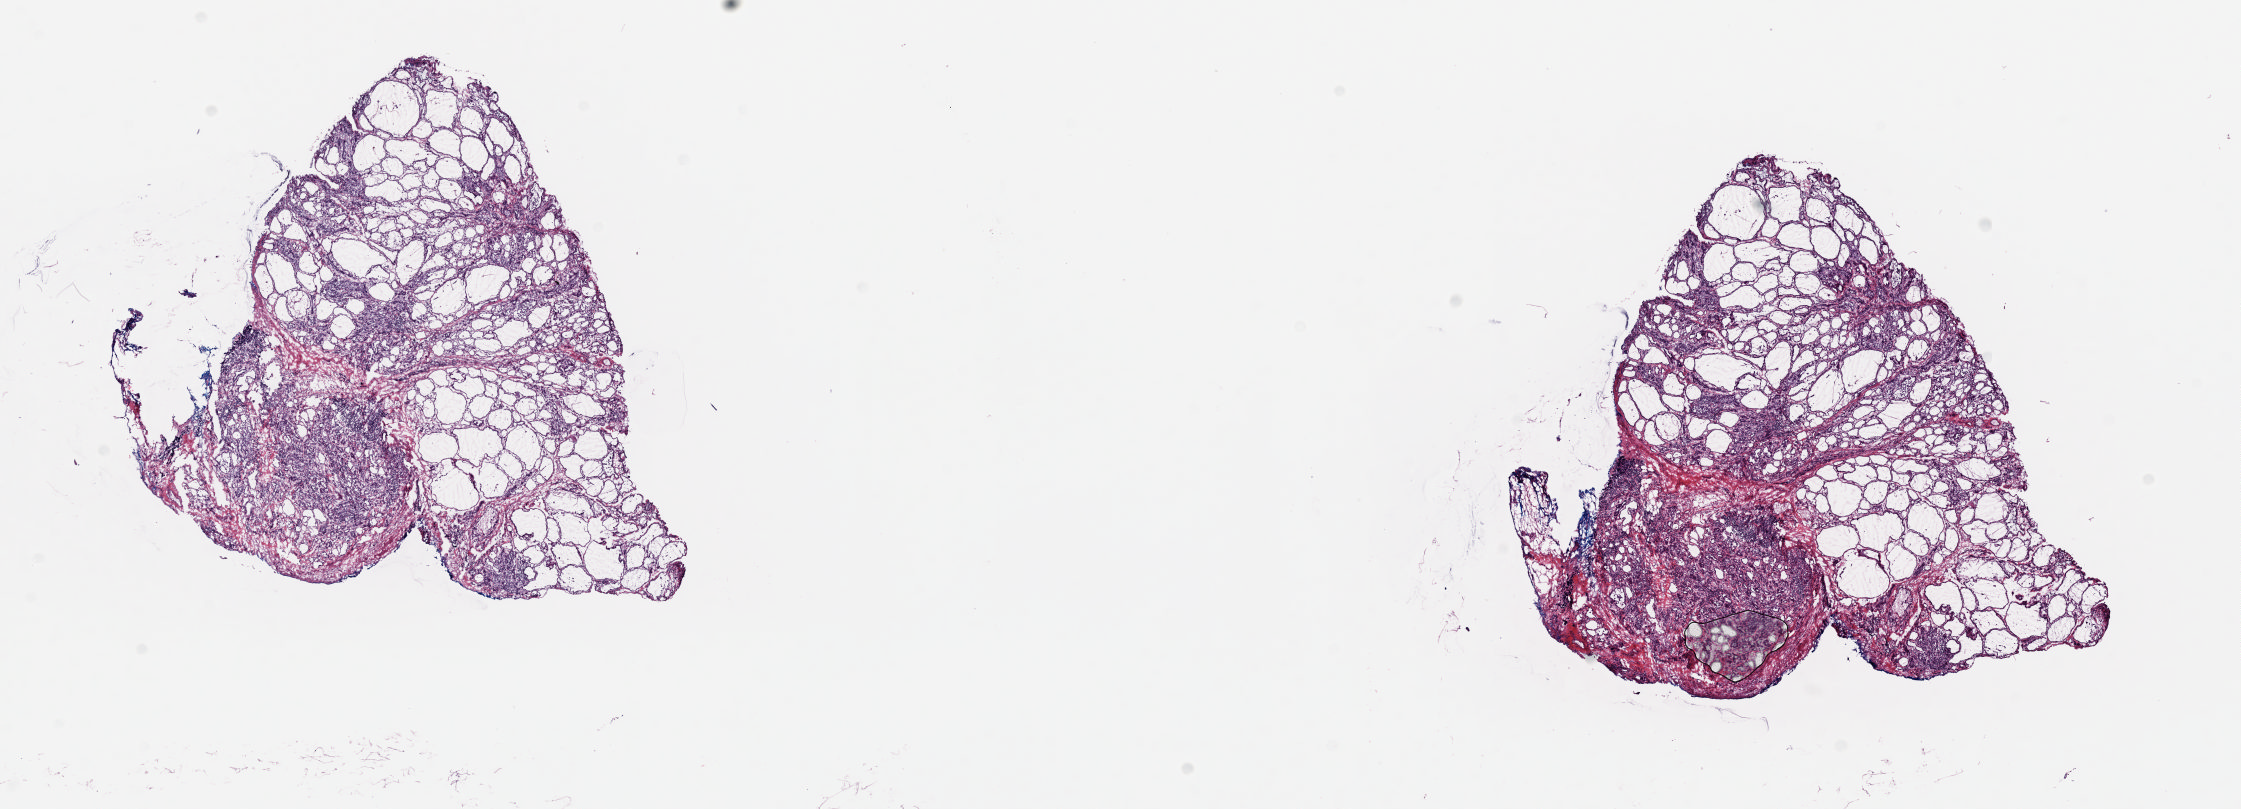
Whole-slide histology image, H&E, whole scanned area (about 17.7 x 6.4 mm) shown as a low-resolution overview; frozen section from the top of the tissue portion; thyroid, solid tissue normal (non-tumour tissue) sample. Female, age 33 years at initial diagnosis. Slide review estimates, as recorded: tumour cells 0%, tumour nuclei 0%, normal cells 70%, stromal cells 30%, necrosis 0%. Inflammatory infiltration, as recorded: lymphocyte infiltration 20%, monocyte infiltration 0%, neutrophil infiltration 0%.
This section: solid tissue normal sample (biorepository sample class). Patient diagnosis: Papillary adenocarcinoma, NOS.